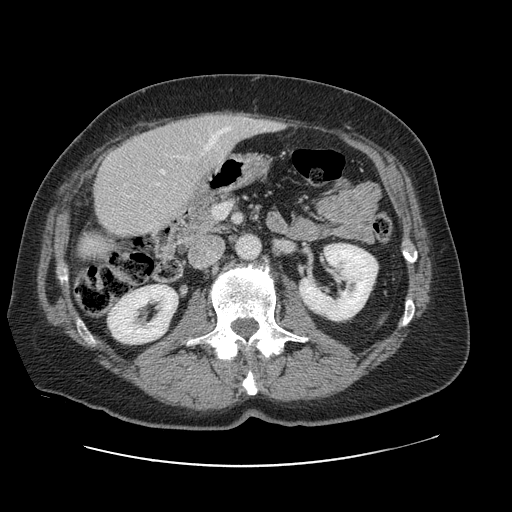
Contrast-enhanced abdominal CT, one axial slice; slice 34 of 138 in the series (ordered by position); 120 kVp; intravenous contrast given; soft-tissue window (W 400 / L 40 HU); 512 × 512 image matrix, field of view 402 × 402 mm. Male patient, age 71 years. Case-level facts recorded for this patient, not image findings: diagnosis: colorectal cancer liver metastases, imaged before liver resection; multiple liver metastases: no; largest metastasis: 3.3 cm; chemotherapy before resection: no.
Outlined on this slice (outlined manually by an expert reader):
- hepatic veins: box from (x=202, y=127) to (x=230, y=155) px
- liver: (x=79, y=114)–(x=274, y=260)
- planned liver remnant (the part of the liver to remain after resection): (x=79, y=133)–(x=189, y=259)
- portal vein (with intrahepatic branches): (x=161, y=170)–(x=165, y=174)